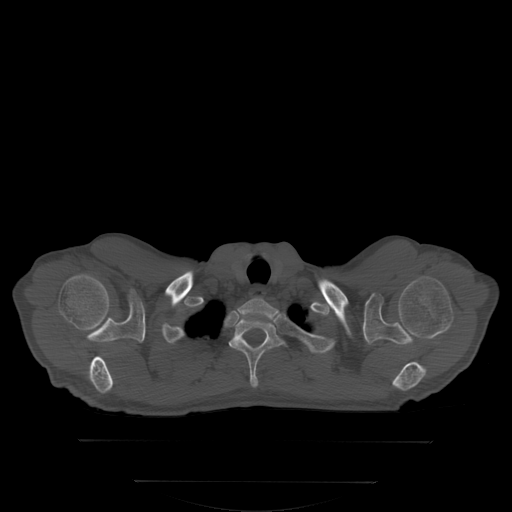
CT including the spine, one axial slice. Slice 288 of 350 in the series (ordered by position). Bone window (W 1800 / L 400 HU). 512 × 512 image matrix. Patient: male, 58 years. Case-level facts recorded for this patient, not image findings: primary cancer: prostate.
Annotated regions visible in this slice (semi-automatic segmentation, software-assisted and operator-edited):
- T1 vertebra: bounding box (x1, y1, x2, y2) in pixels: (229, 320, 288, 386)